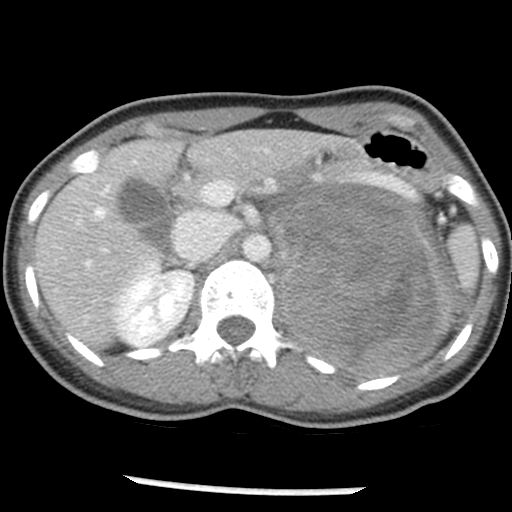
Contrast-enhanced abdominal CT, one axial slice; slice 29 of 54 in the series (ordered by position); reconstruction kernel STANDARD; intravenous contrast given; soft-tissue window (W 400 / L 40 HU); 5 mm slice thickness; 512 × 512 image matrix. Female patient, age 33 years. From the clinical record (not read from this slice): diagnosis: adrenocortical carcinoma; tumour side: left adrenal; tumour size at pathology: 11 cm; Ki-67 index: 20 %; stage (as recorded): 2.
Structures marked on this image (semi-automatic segmentation, software-assisted and operator-edited):
- mass: bounding box <266,185,453,373> (left, top, right, bottom; pixels)